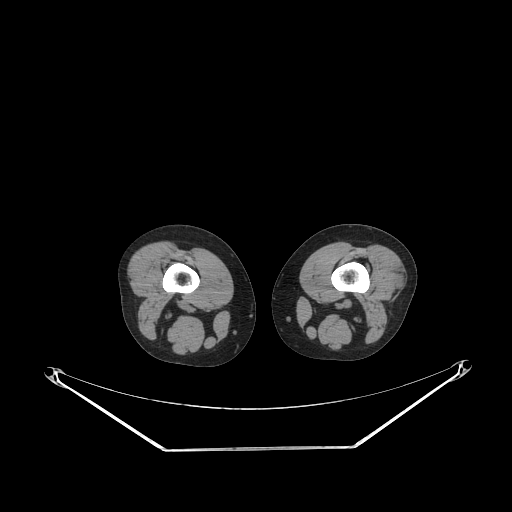
CT of an extremity soft-tissue mass (from a PET/CT study), one axial slice; slice 181 of 223 in the series (ordered by position); reconstruction kernel STANDARD; 140 kVp; soft-tissue window (W 400 / L 40 HU); 512 × 512 image matrix, field of view 500 × 500 mm. Female patient. From the clinical record (not read from this slice): histological type: spindle cell suggestive of biphasic synovial sarcoma; grade: intermediate; site of the primary tumour: left knee.
Structures marked on this image (expert contour drawn on MRI and transferred to this co-registered scan by the dataset authors):
- gross tumour volume including surrounding oedema: box from (x=383, y=253) to (x=405, y=289) px
- gross tumour volume (mass): (x=383, y=253)–(x=405, y=289)